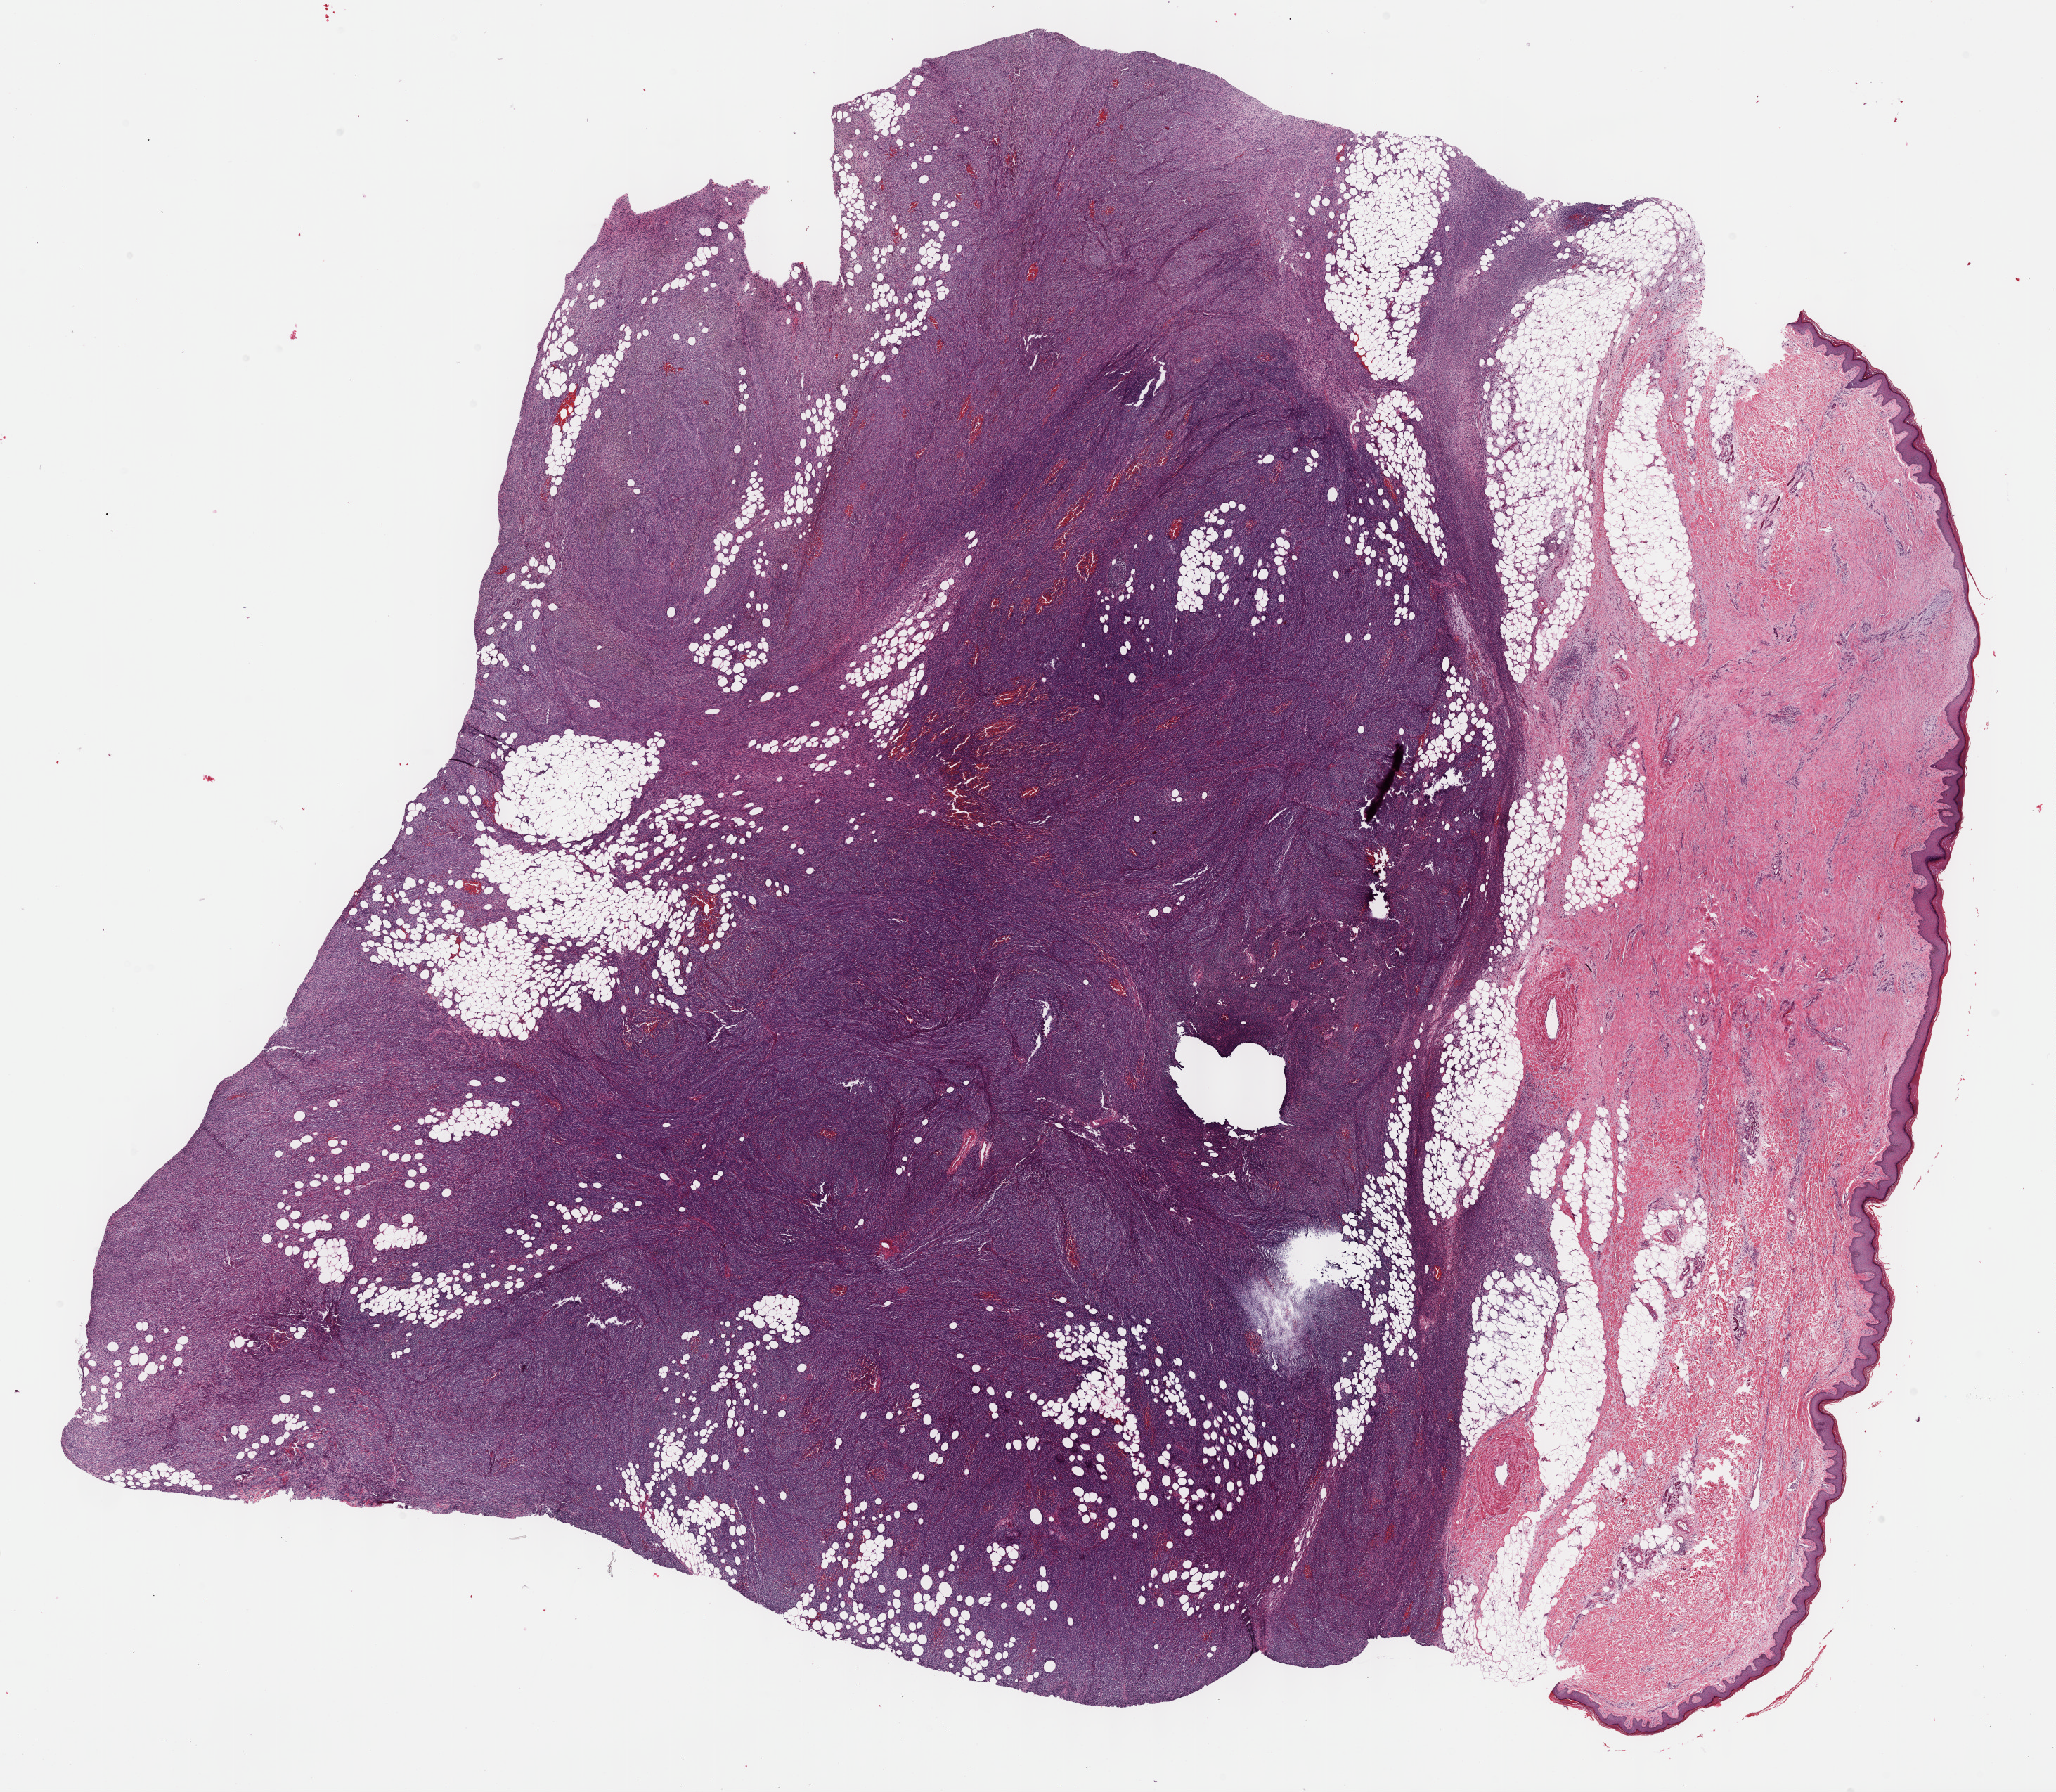
Whole-slide histology image, Hematoxylin and eosin (H&E) stained, a low-resolution overview of the entire scanned area, about 23.7 x 20.6 mm (from a 40x scan). FFPE section. Sample: primary tumour, connective, subcutaneous and other soft tissues. Patient: female, age at initial diagnosis 28 years.
• pathologic diagnosis: Synovial sarcoma, spindle cell (connective, subcutaneous and other soft tissues of lower limb and hip)